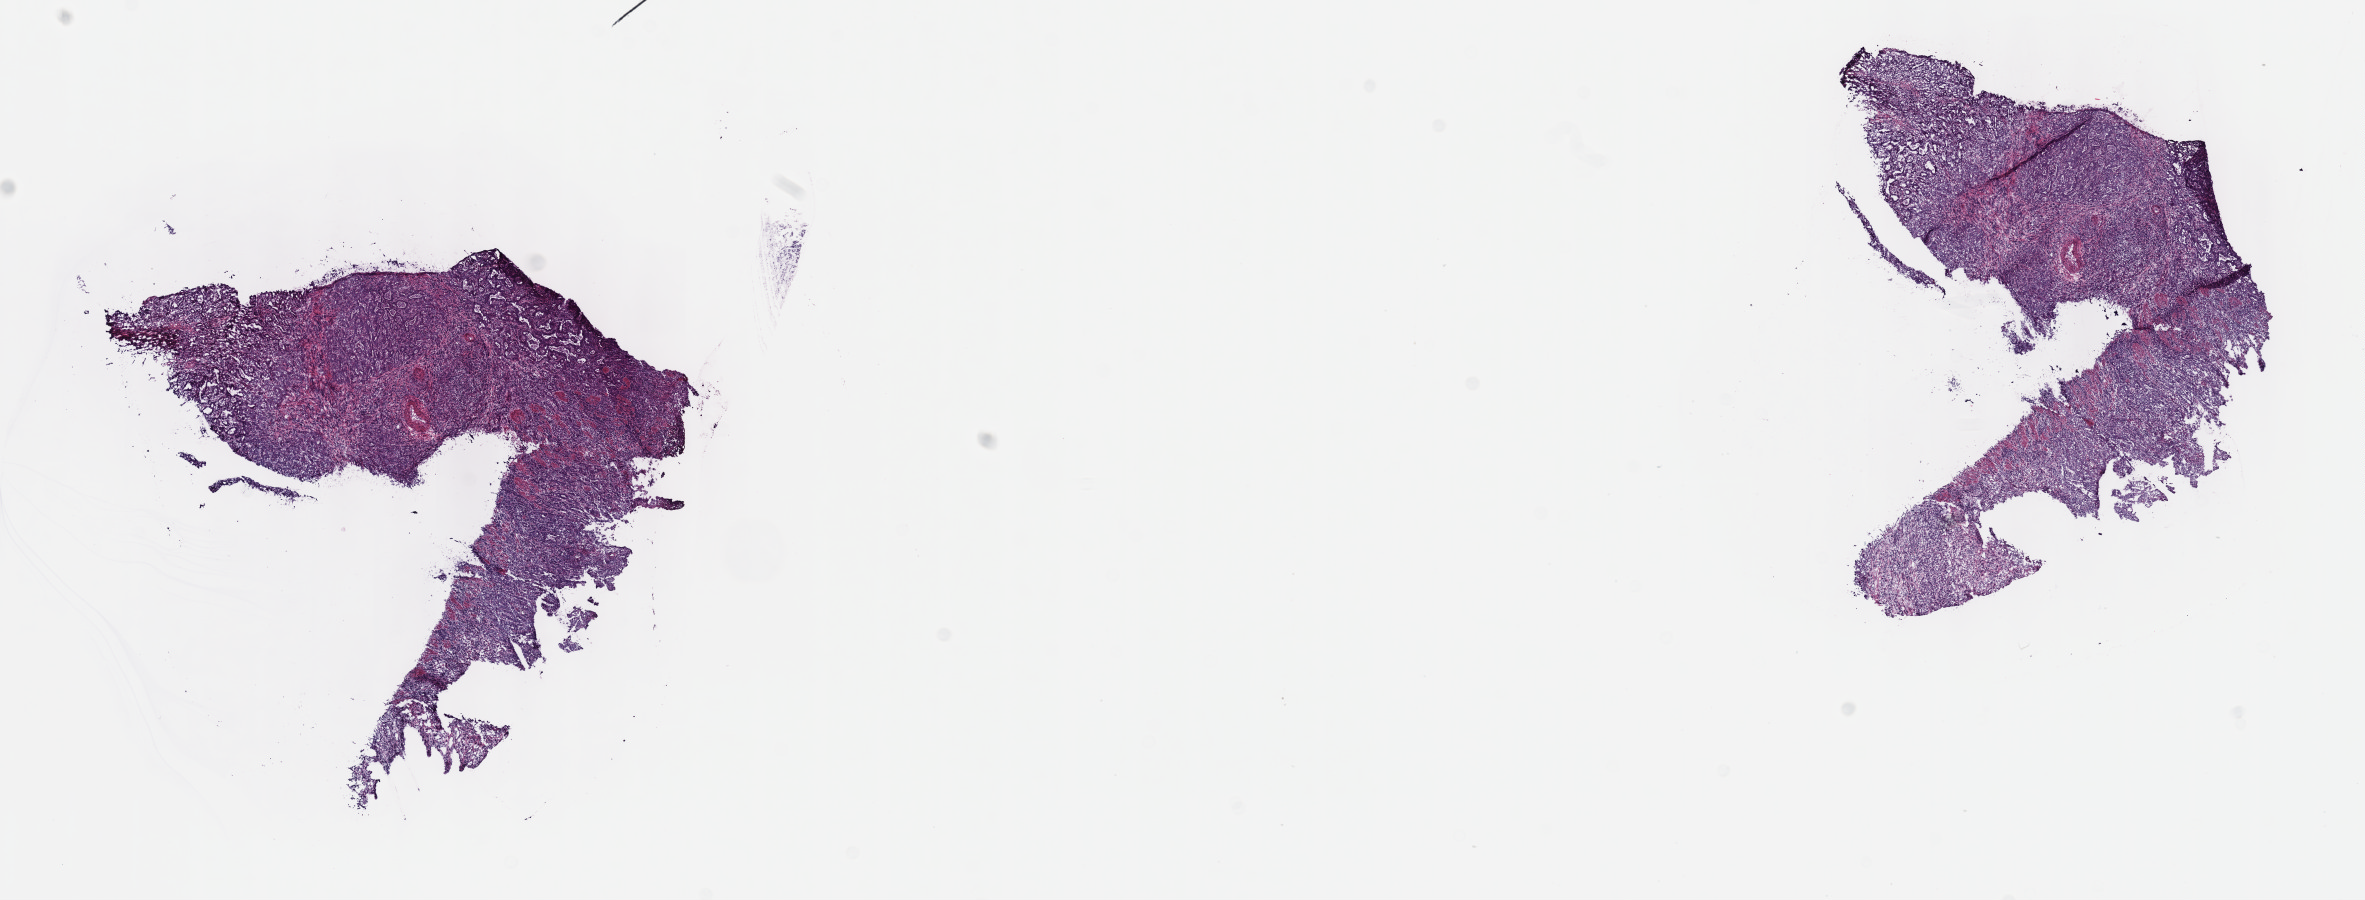
Digitized H&E-stained tissue section (whole slide) — a low-resolution overview of the entire scanned area, about 19.1 x 7.3 mm; frozen section from the top of the tissue portion; esophagus, primary tumour sample. Patient: male, age at initial diagnosis 75 years. Histologic grade: G3 (poorly differentiated). Slide review estimates, as recorded: tumour cells 80%, tumour nuclei 80%, normal cells 0%, stromal cells 15%, necrosis 5%. Inflammatory infiltration, as recorded: lymphocyte infiltration 40%, monocyte infiltration 20%, neutrophil infiltration 20%.
Diagnosis: Adenocarcinoma, NOS (cardia, NOS). AJCC pathologic stage: IIB (7th edition).